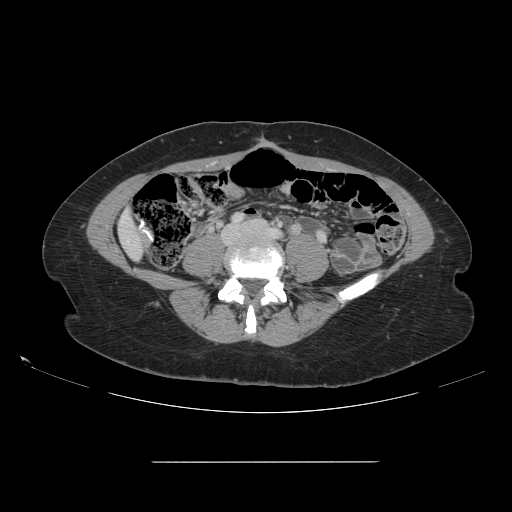
Contrast-enhanced abdominal CT, one axial slice. Position 11 of 151 along the scan axis. 120 kVp. Intravenous contrast given. Soft-tissue window (W 400 / L 40 HU). 2.5 mm slice thickness. 512 × 512 image matrix, field of view 421 × 421 mm. Female patient, age 46 years. Case-level facts recorded for this patient, not image findings: diagnosis: colorectal cancer liver metastases, imaged before liver resection; multiple liver metastases: yes; largest metastasis: 3 cm; chemotherapy before resection: no.
Annotated regions visible in this slice (expert manual segmentation):
- liver: box from (x=119, y=213) to (x=144, y=258) px
- planned liver remnant (the part of the liver to remain after resection): (x=120, y=214)–(x=144, y=258)